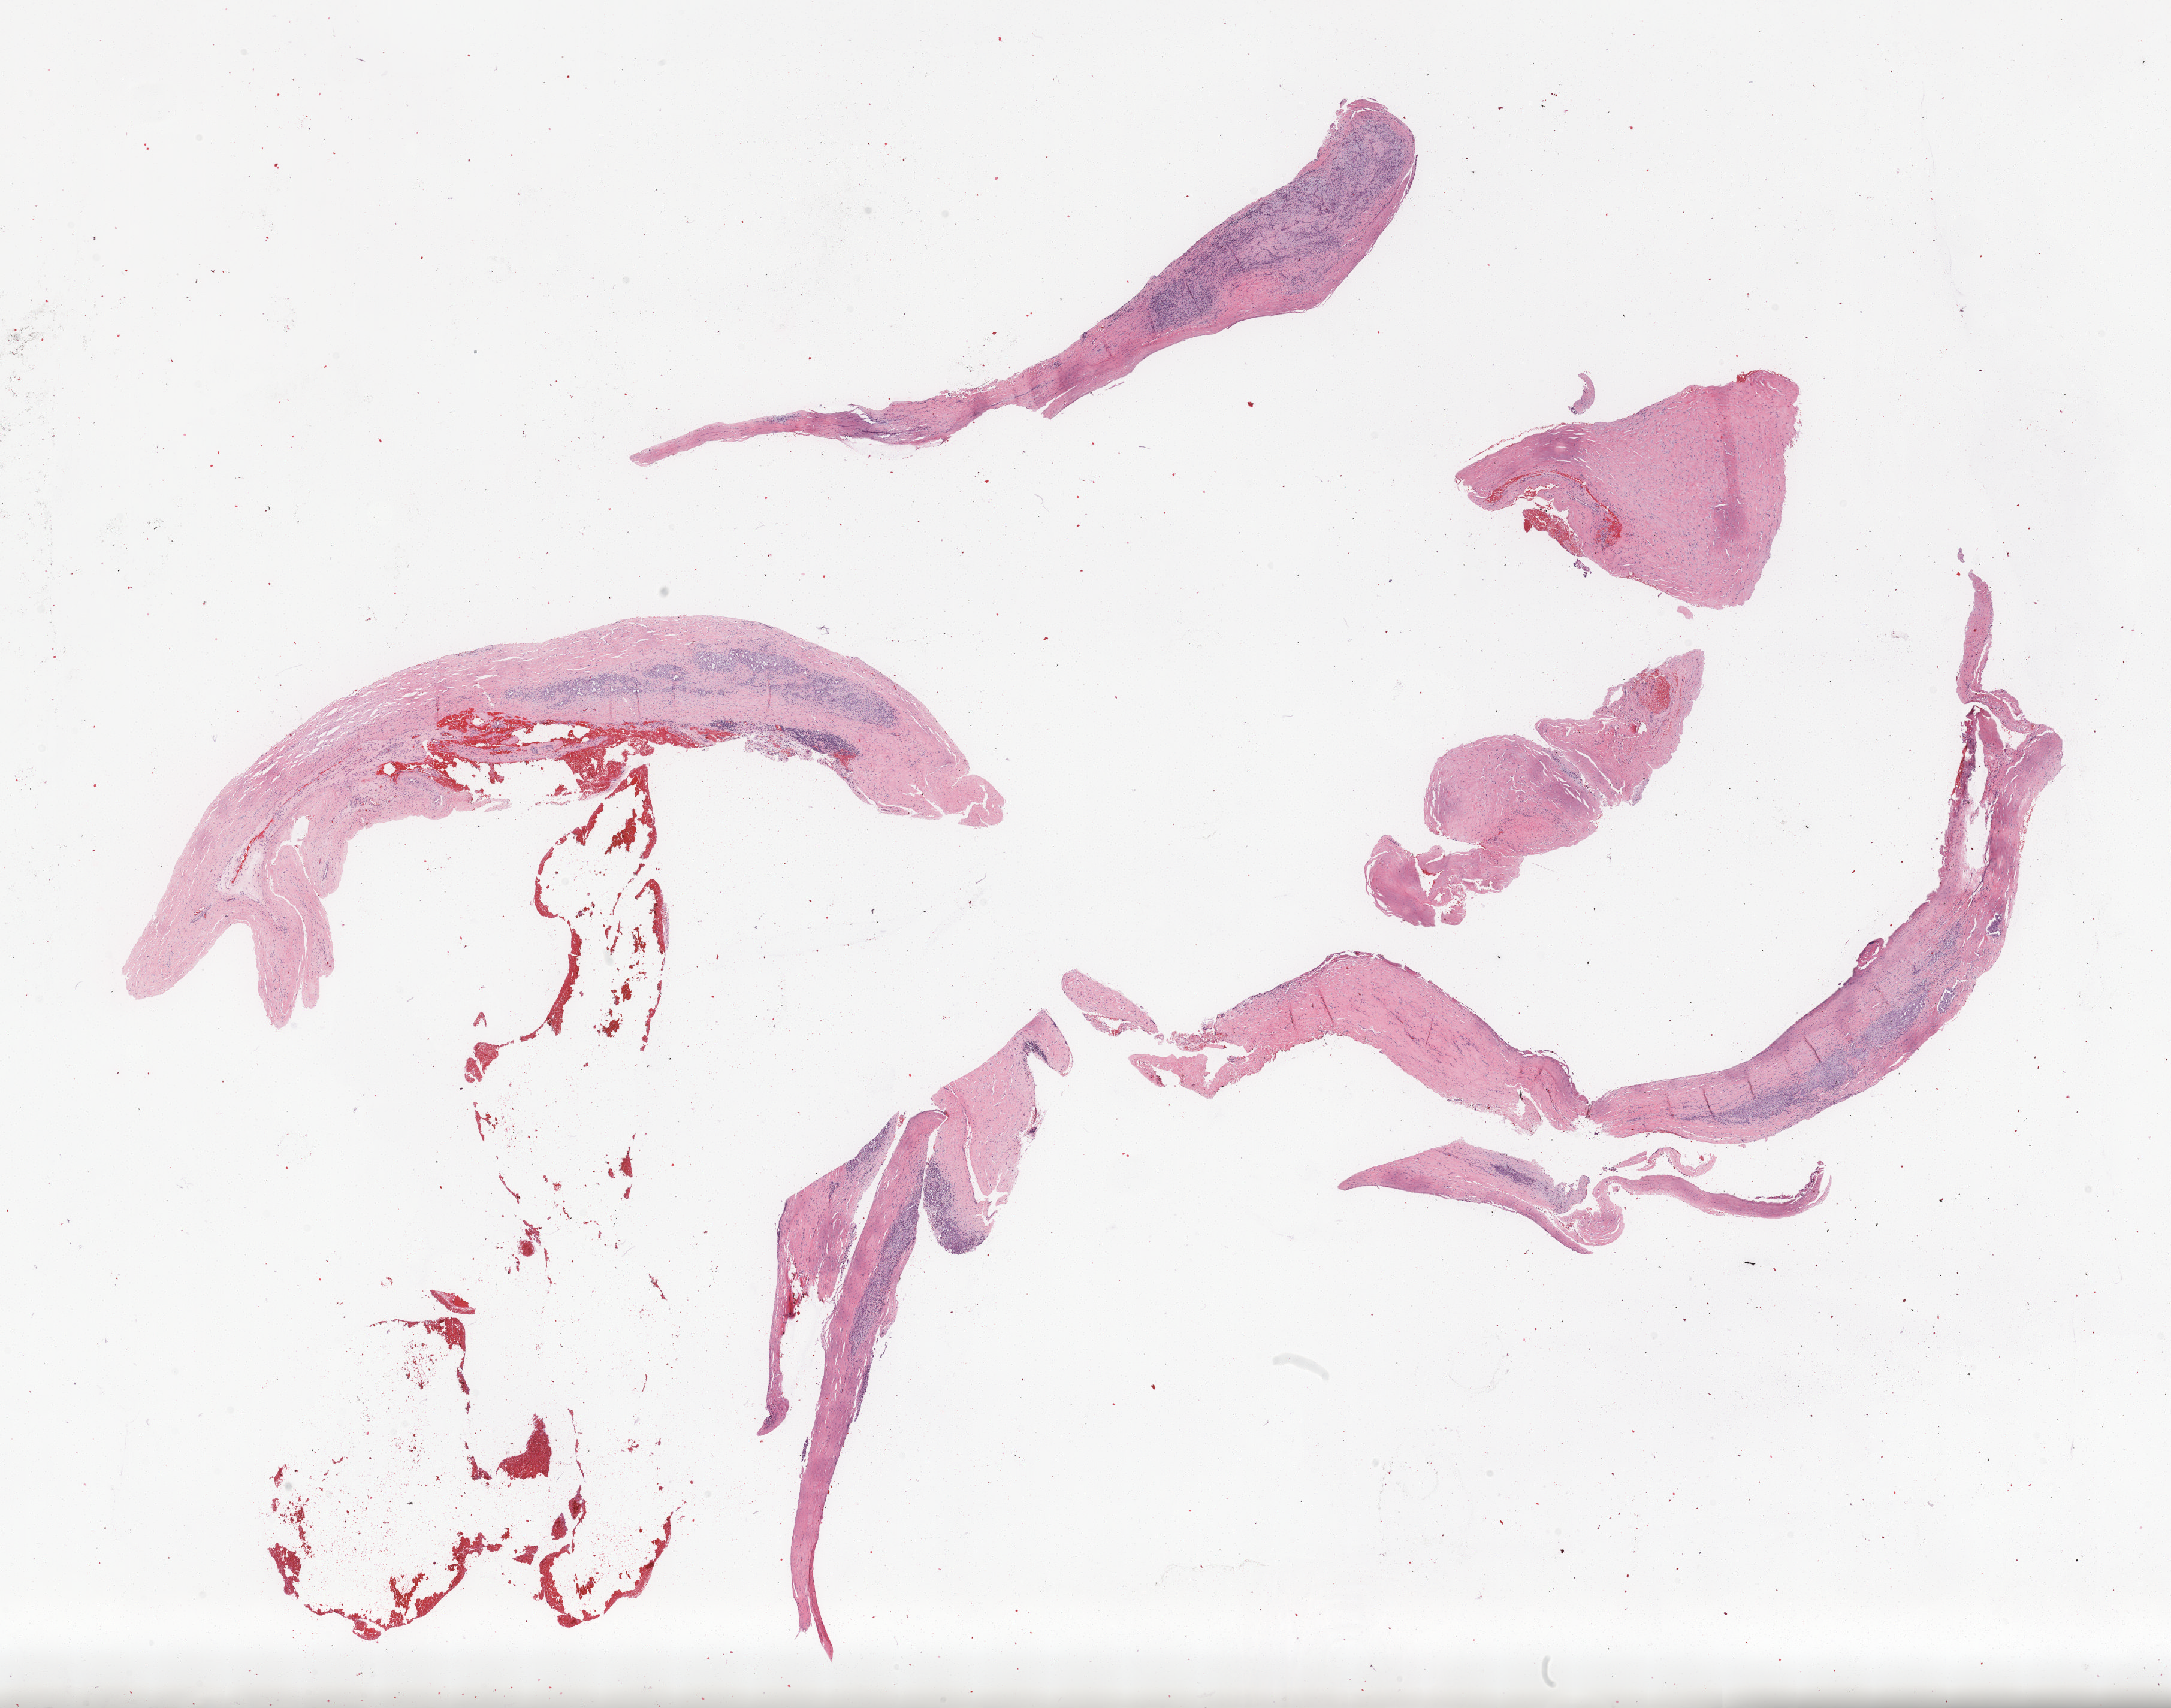
Digitized H&E tissue section (whole slide), low-resolution overview of the scanned area, about 29.1 x 22.9 mm (acquisition: 20x scan), formalin-fixed paraffin-embedded (FFPE) diagnostic section, mesothelium, primary tumour sample. Patient: female, age at initial diagnosis 64 years.
* diagnosis: Epithelioid mesothelioma, malignant (pleura, NOS)
* AJCC pathologic stage: IV (7th edition)
* laterality: left